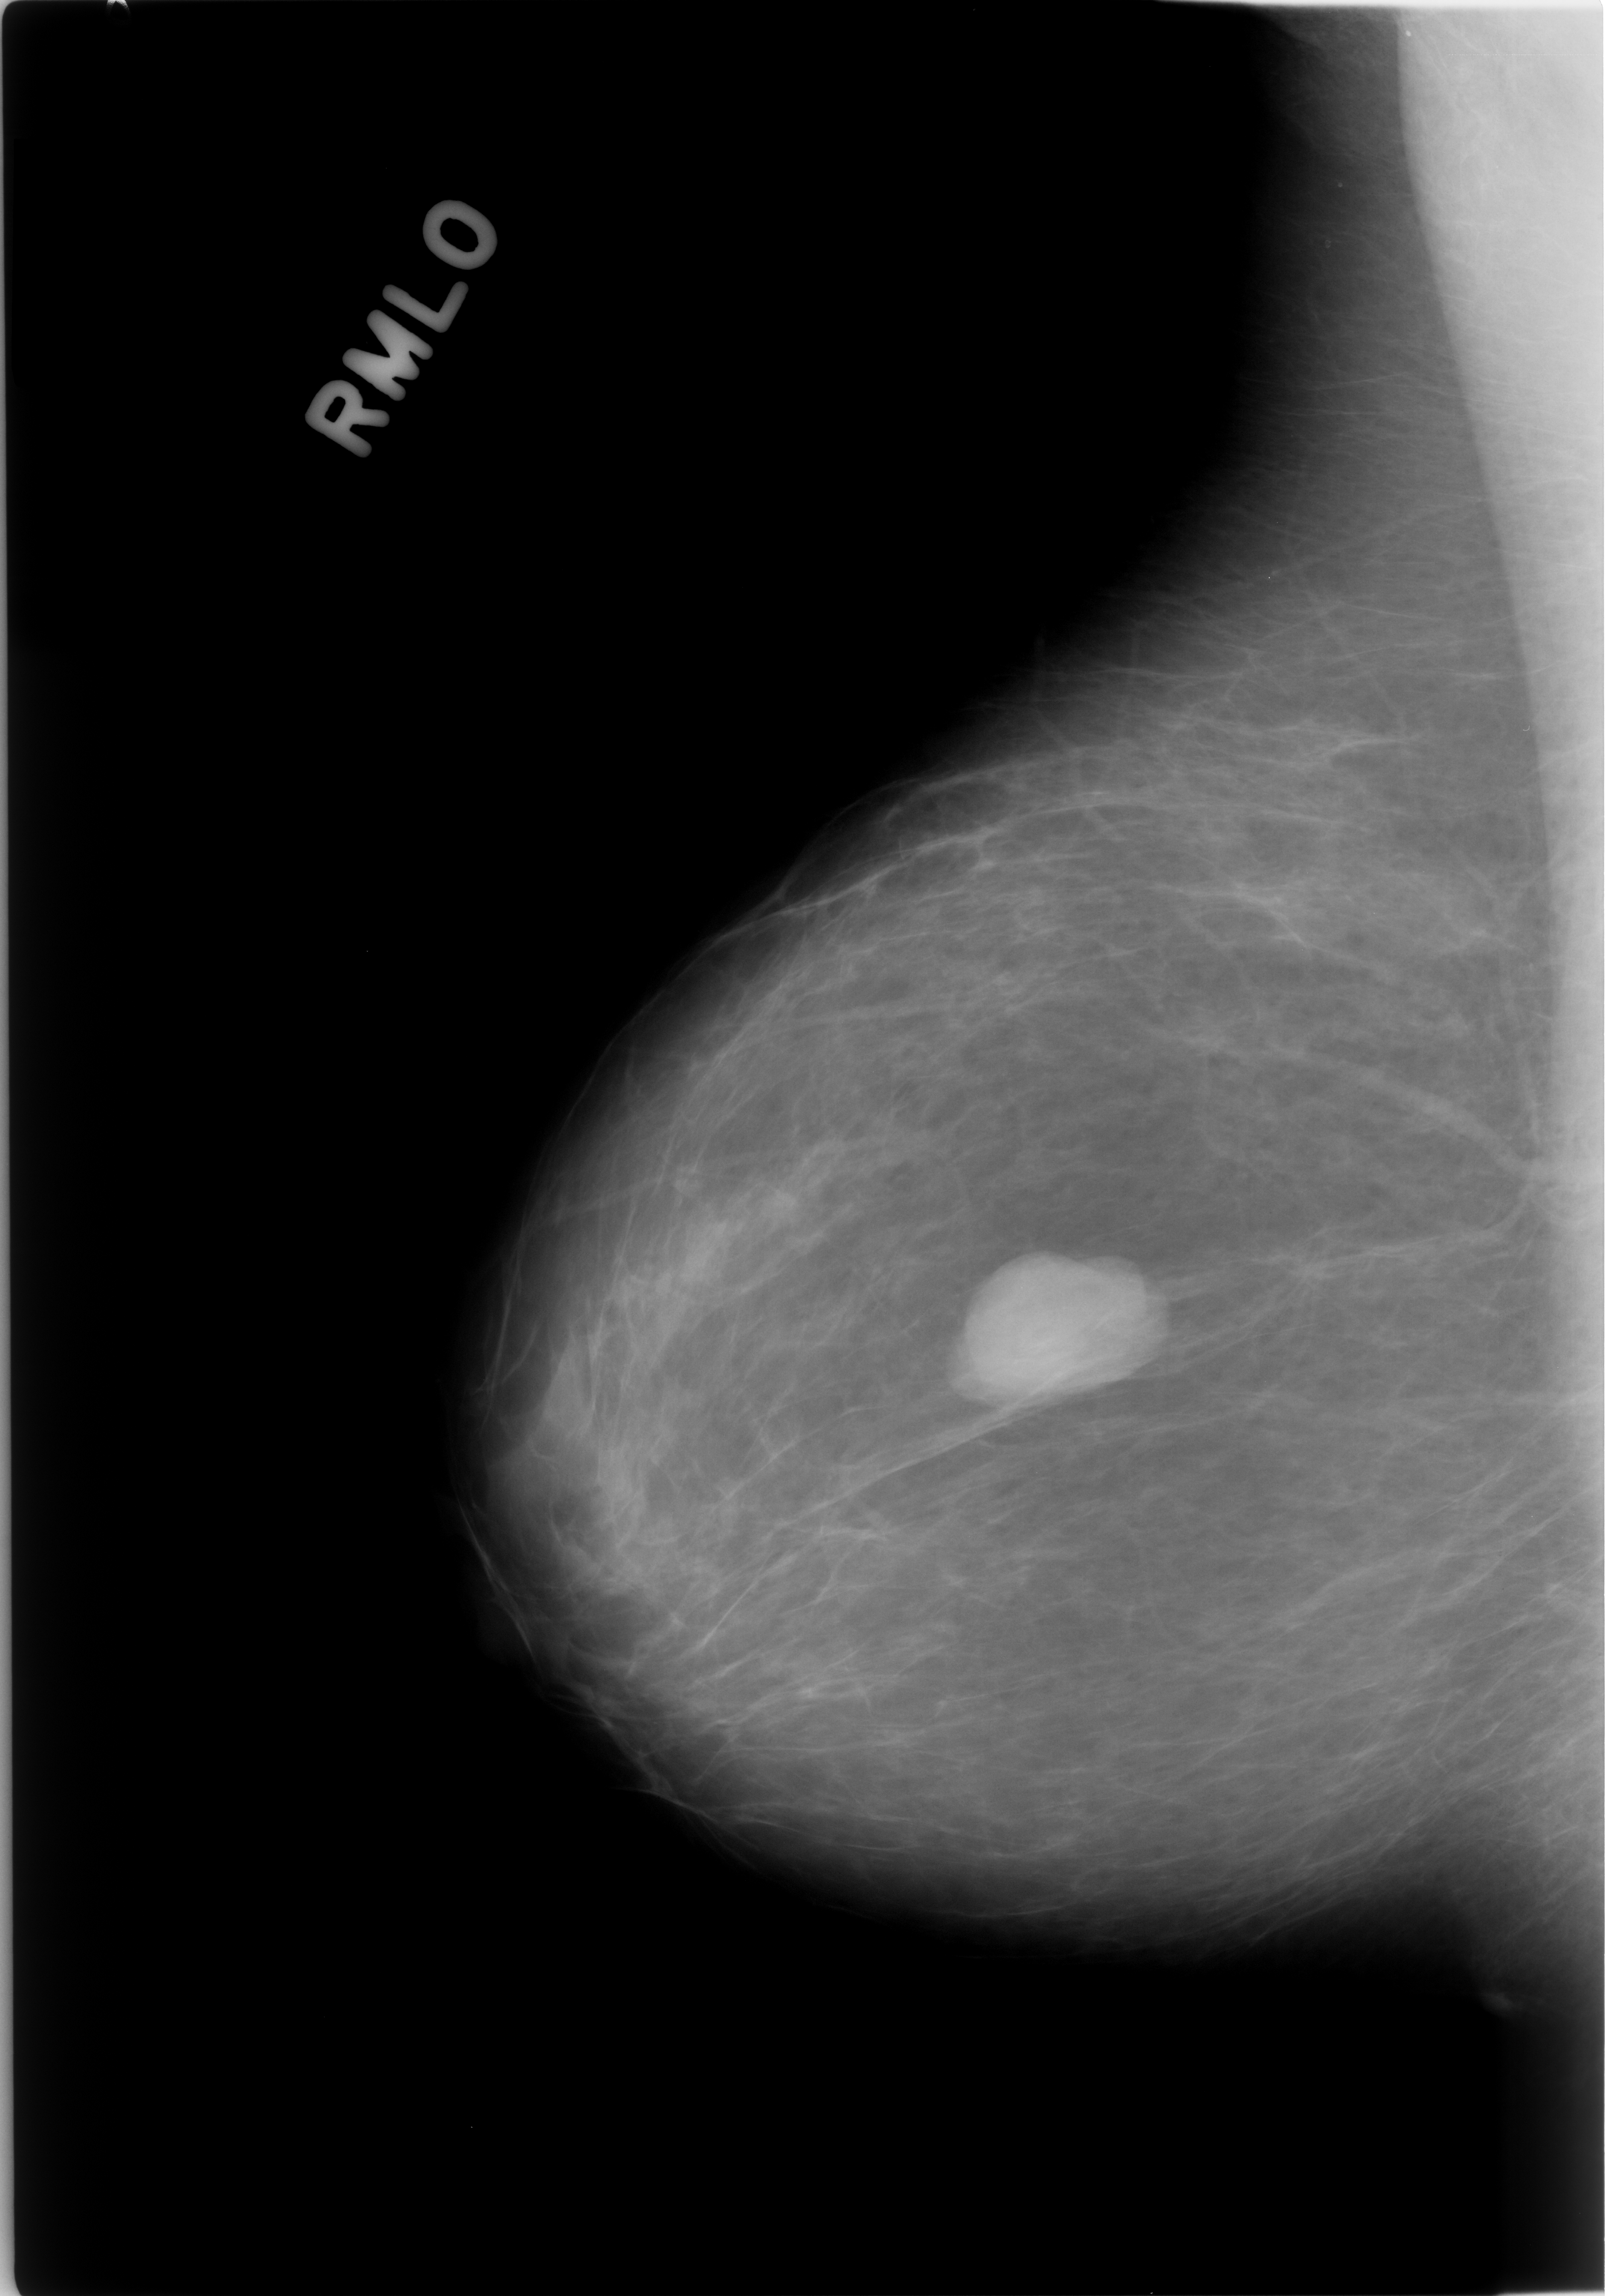
Digitized screen-film mammogram, right breast, MLO view.
Marked findings (only marked abnormalities are described; nothing is implied about the rest of the image): mass, shape lobulated, margins circumscribed; BI-RADS assessment category 4; subtlety rating 5 on a 1 (subtle) to 5 (obvious) scale; pathology (as recorded): benign.